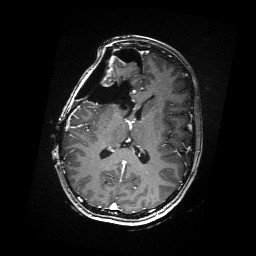
Brain MRI from a brain-tumour surgery series, one axial slice; position 83 of 176 along the scan axis; T1-weighted post-contrast; 1 mm slice thickness; 256 × 256 image matrix, field of view 256 × 256 mm. Case-level facts recorded for this patient, not image findings: histopathology: Metastatic Carcinoma from Breast primary.
Annotated regions visible in this slice (manually delineated by an expert):
- residual tumour: box from (x=88, y=68) to (x=104, y=86) px